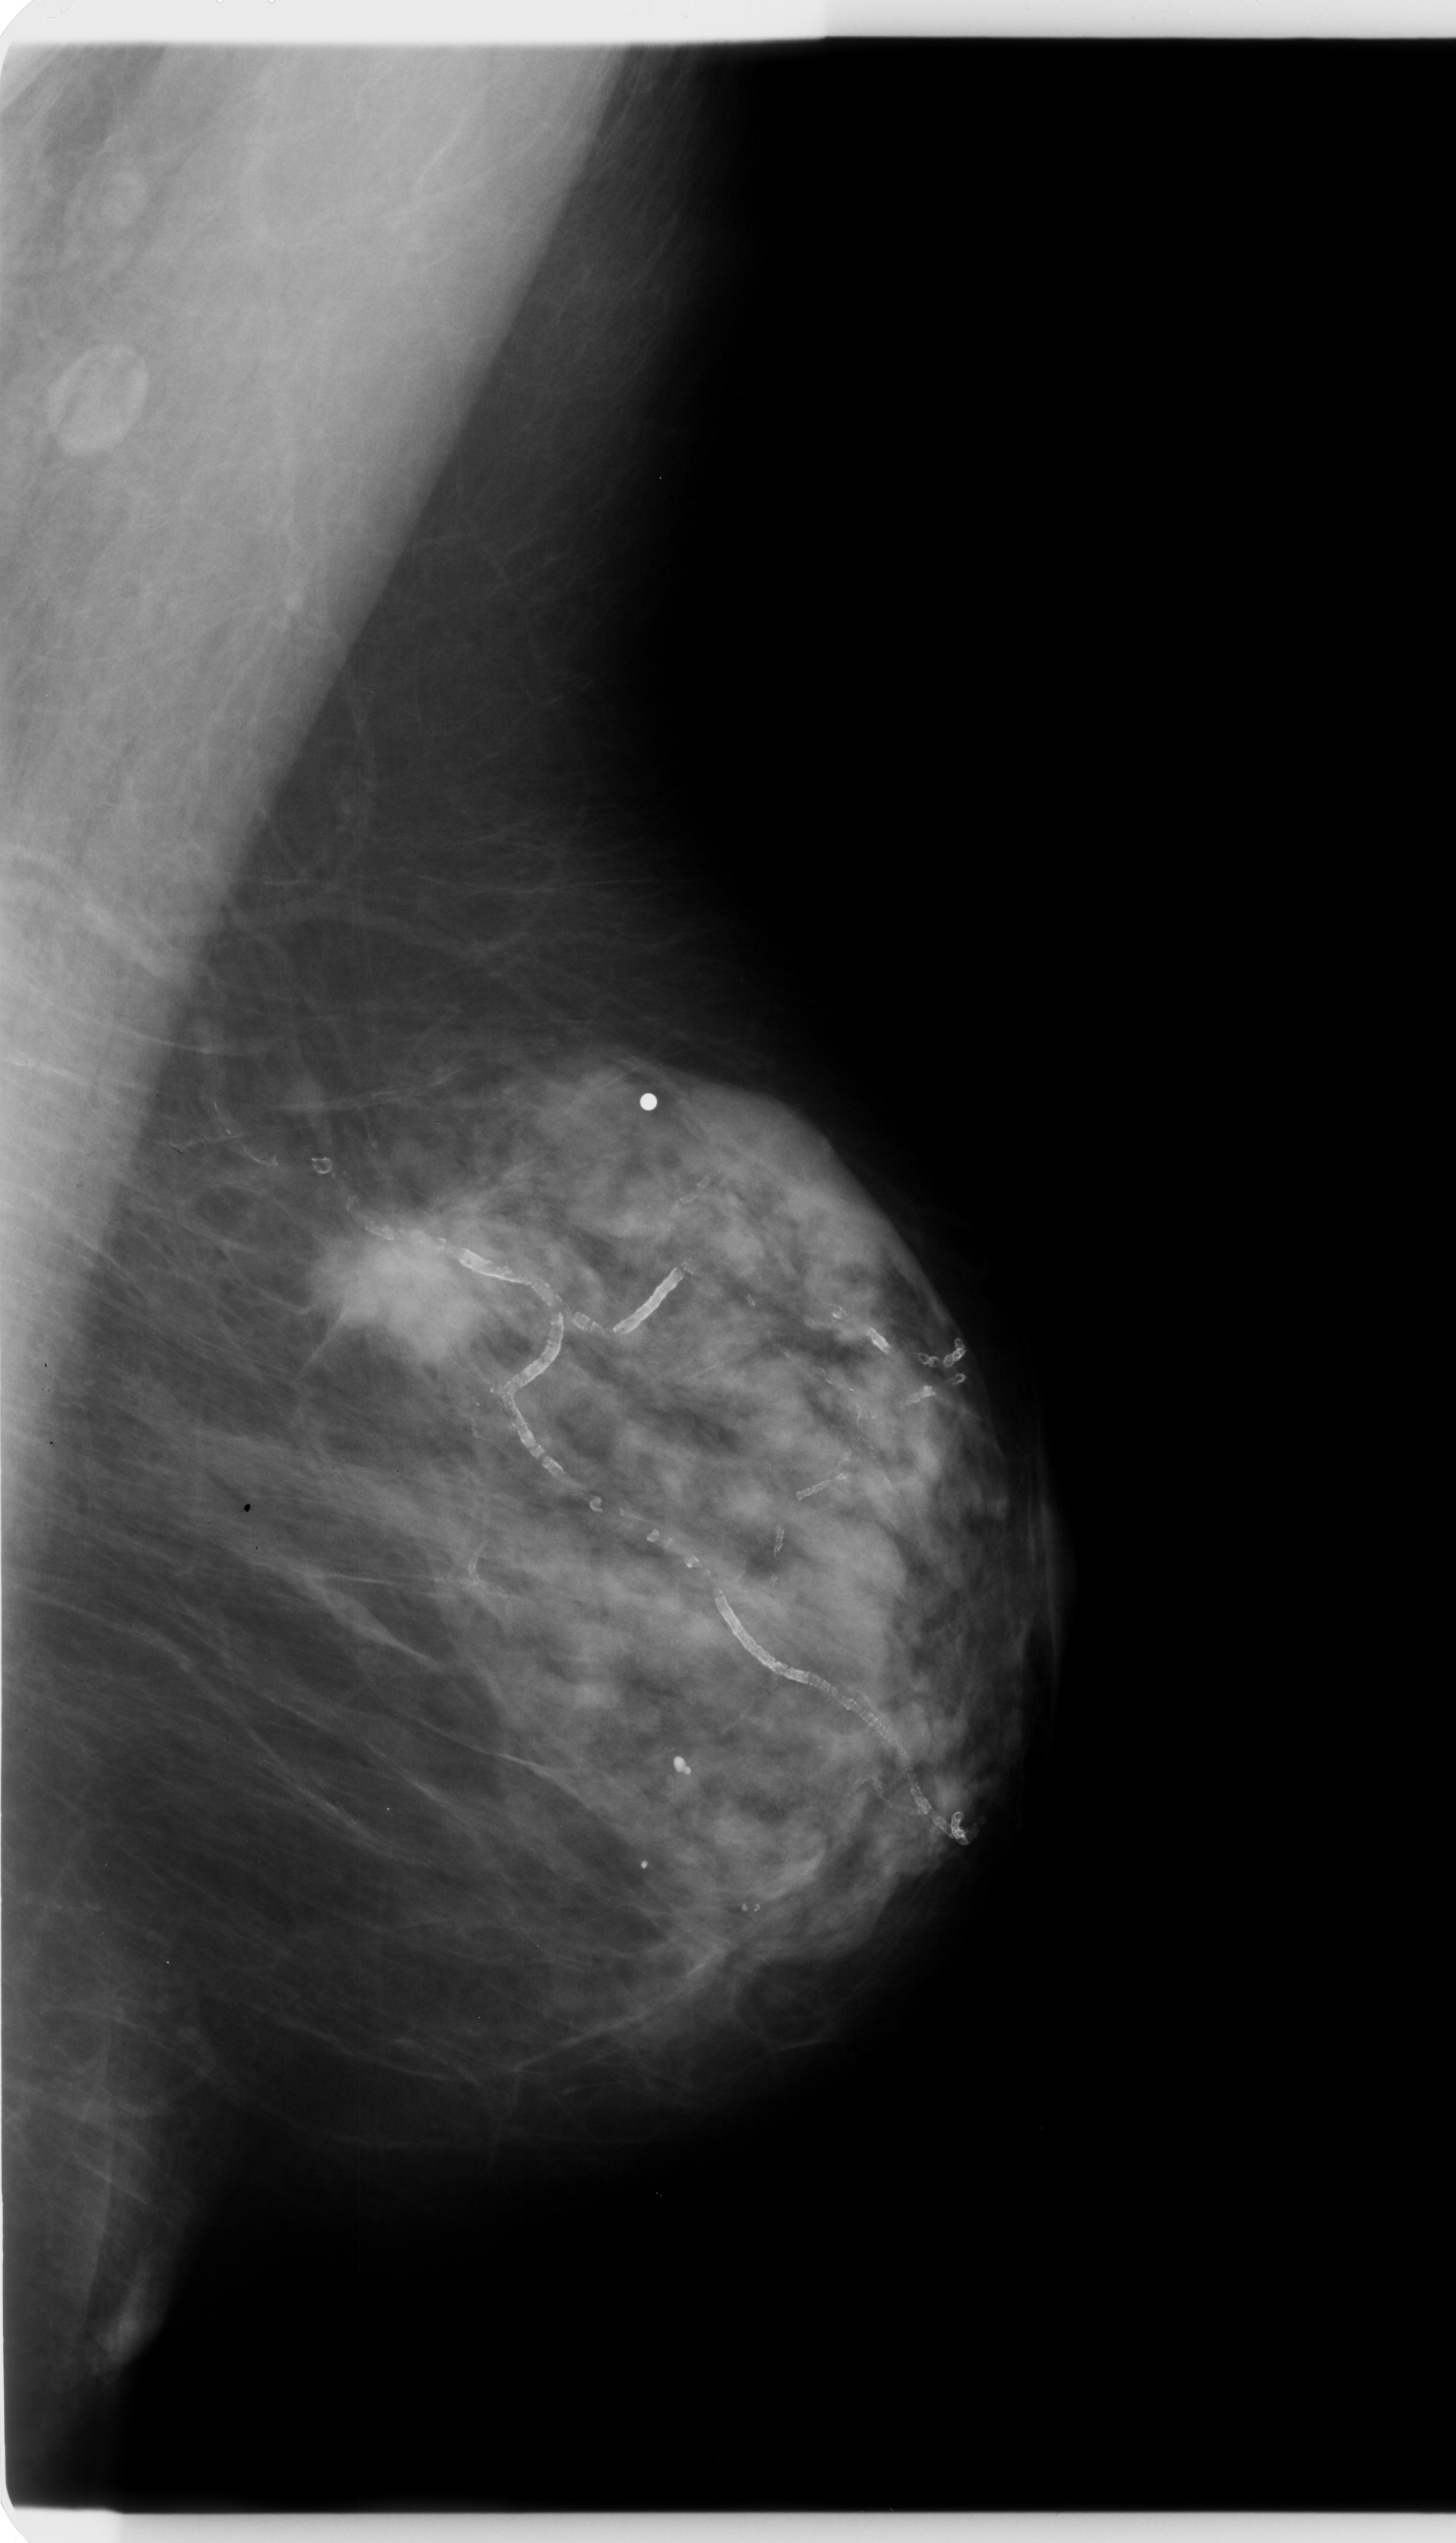
Scanned film-screen mammogram. Left breast. MLO view. BI-RADS breast density category 2 (scale 1–4). 1456 × 2543 image matrix.
Marked abnormalities (boxes around the expert regions of interest):
- mass, shape oval, margins spiculated; BI-RADS assessment category 5; subtlety rating 5 on a 1 (subtle) to 5 (obvious) scale; pathology result (as recorded, not read from the image): malignant: bounding box (x1, y1, x2, y2) in pixels: (253, 1144, 593, 1411)